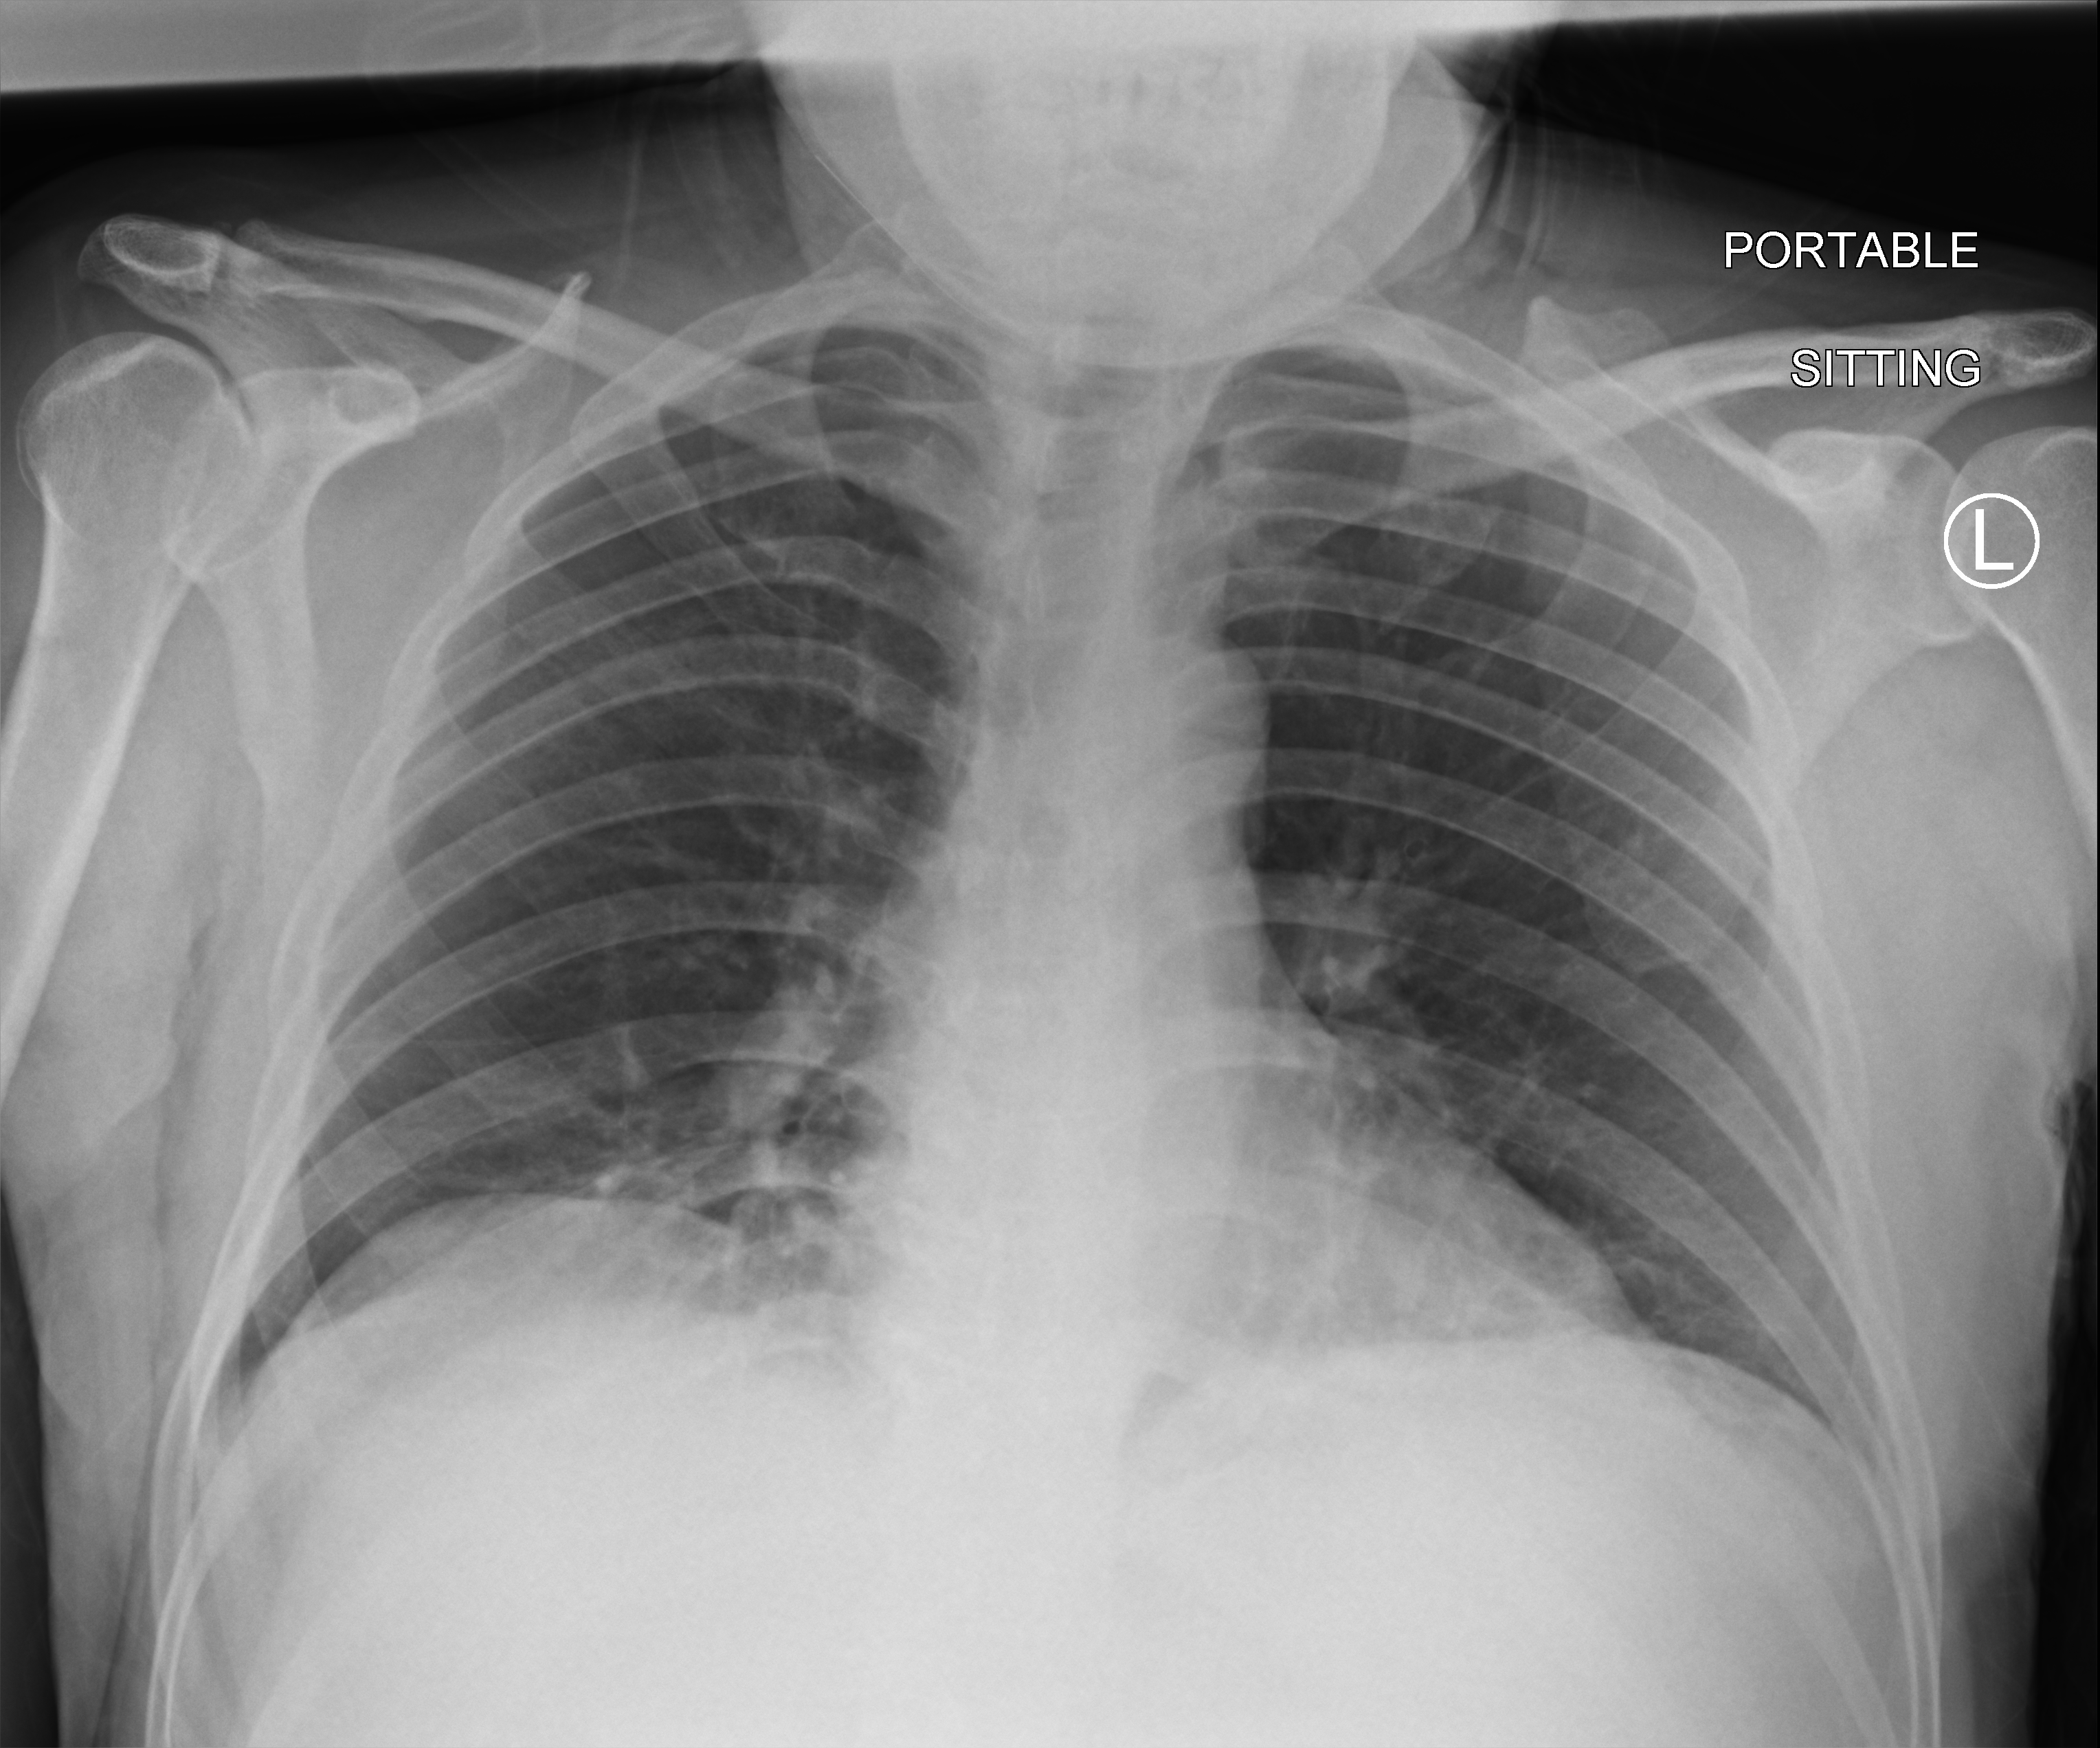
Bedside chest radiograph (computed radiography). Patient hospitalised with COVID-19; male, aged 18–59 years.
From the hospital-stay record, not from the radiograph (when in the stay this image was taken is not recorded): mechanically ventilated during this hospital stay: no; COPD (admission record): no.